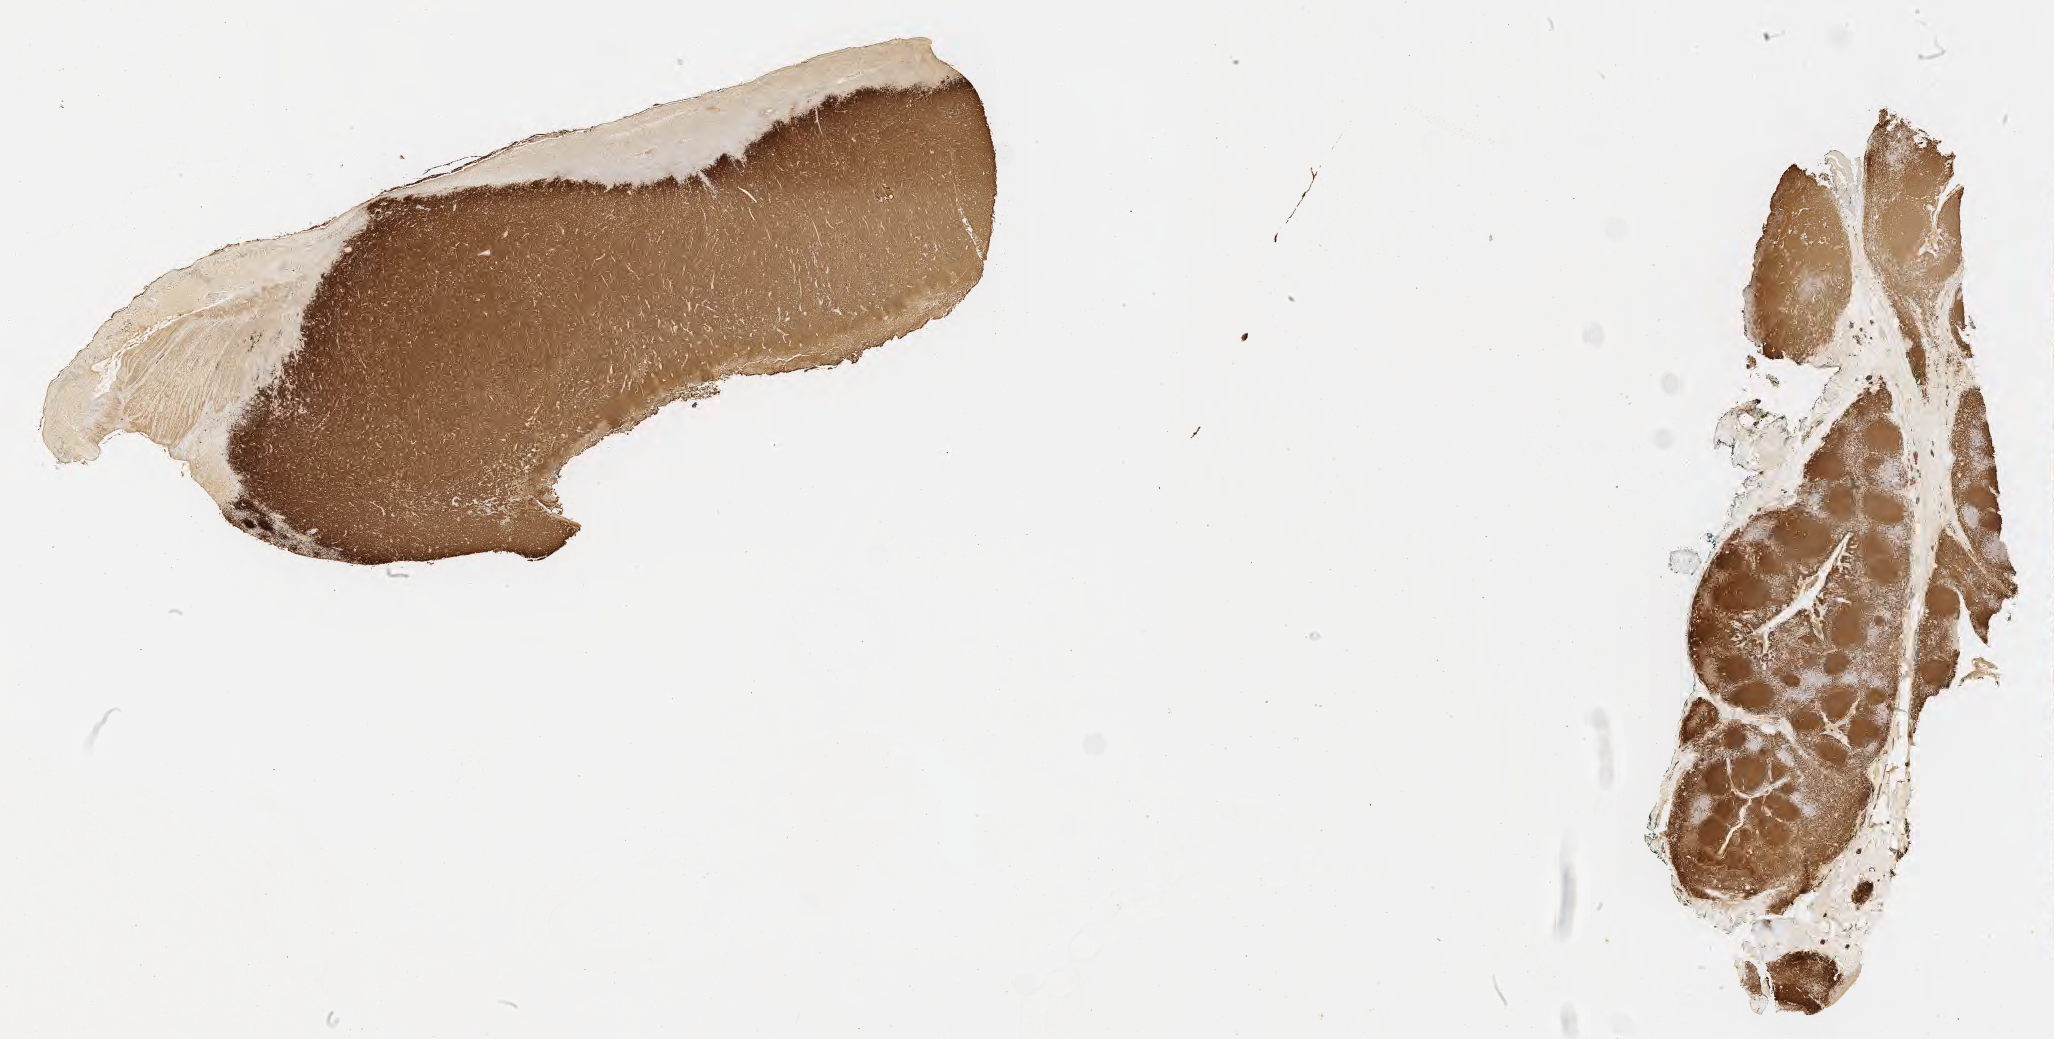
Immunohistochemistry (IHC) whole-slide image stained for CD20 — a low-resolution overview of the entire scanned area, about 33.2 x 16.8 mm. Specimen: tumor tissue. Anatomic site: small intestine. Patient: male, age at initial diagnosis 3 years.
Diagnosis: Burkitt lymphoma, NOS.